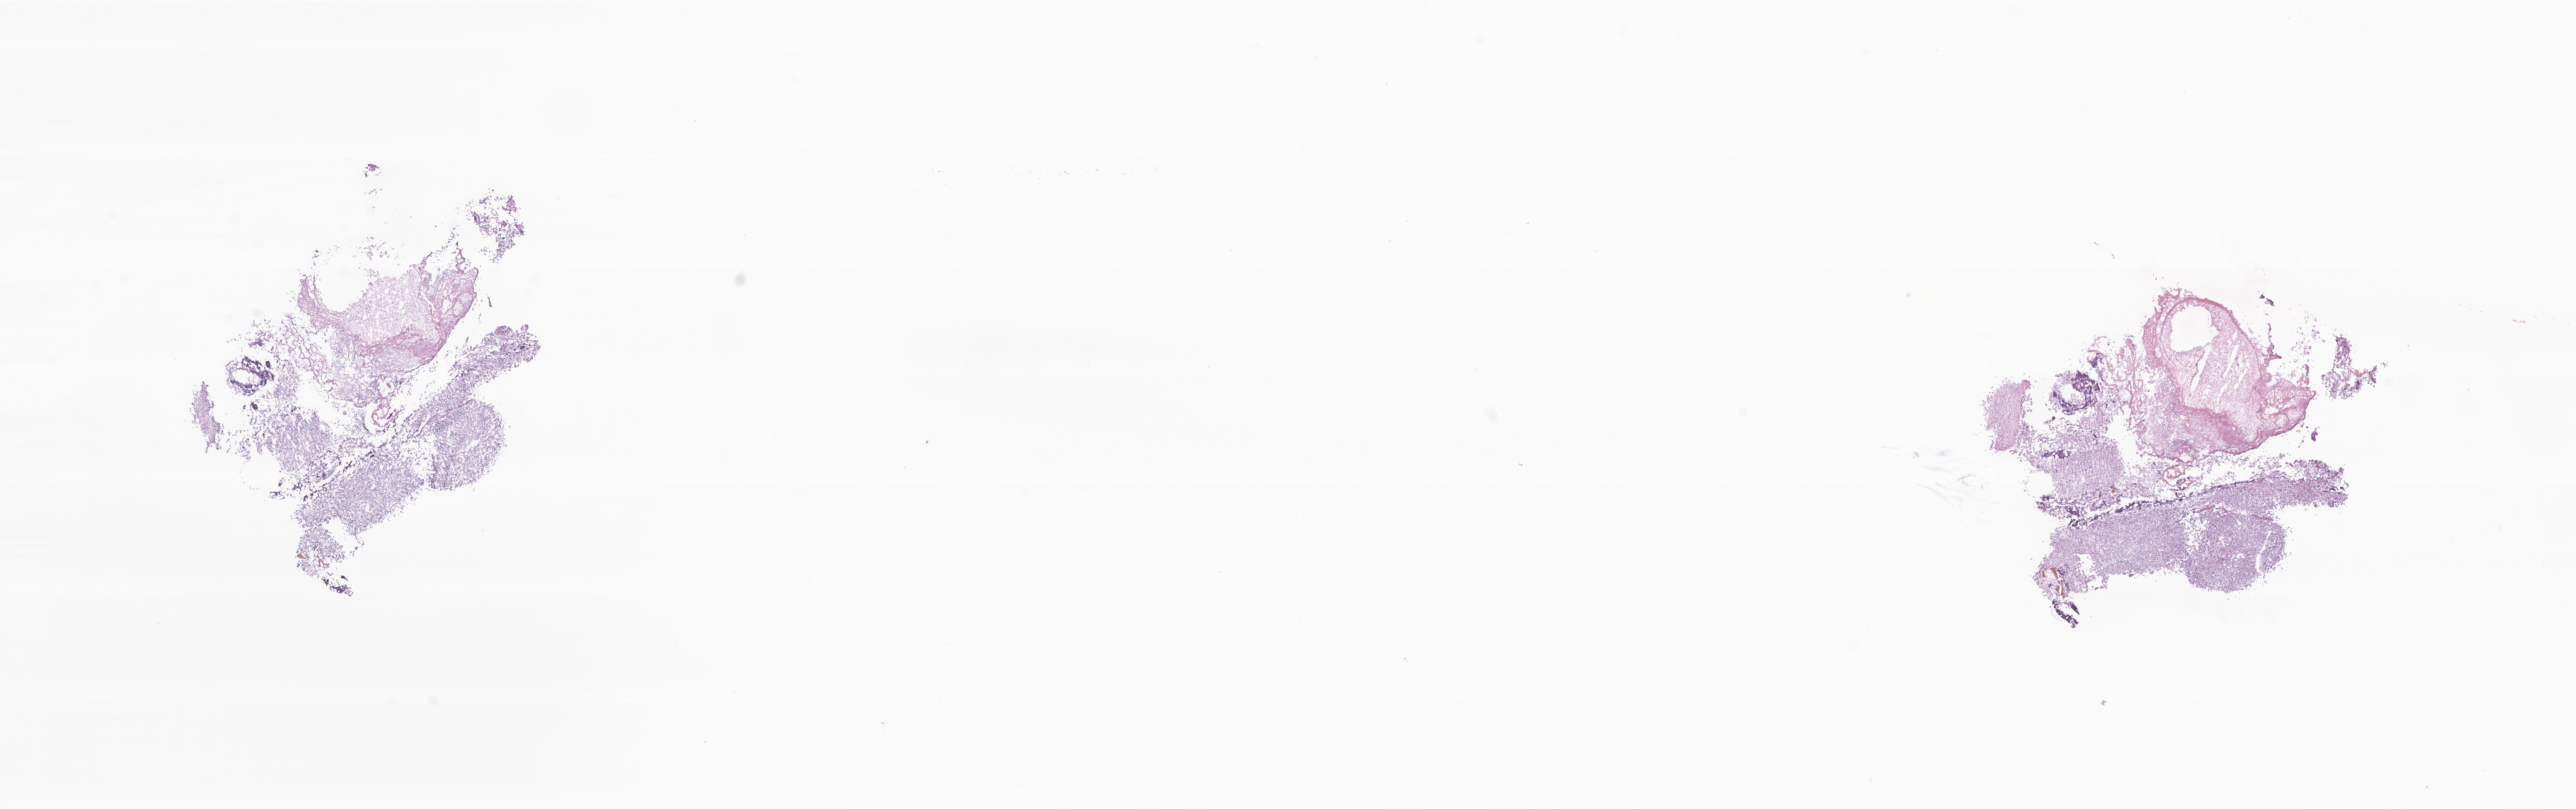
Haematoxylin and eosin whole-slide image of tumor tissue from the brain — a low-resolution overview of the entire scanned area, about 25.3 x 7.9 mm, cryosection (OCT / tissue freezing medium). Male patient, age 175 months (14 years 7 months).
- diagnosis (ICD-O-3 morphology term): Medulloblastoma, NOS